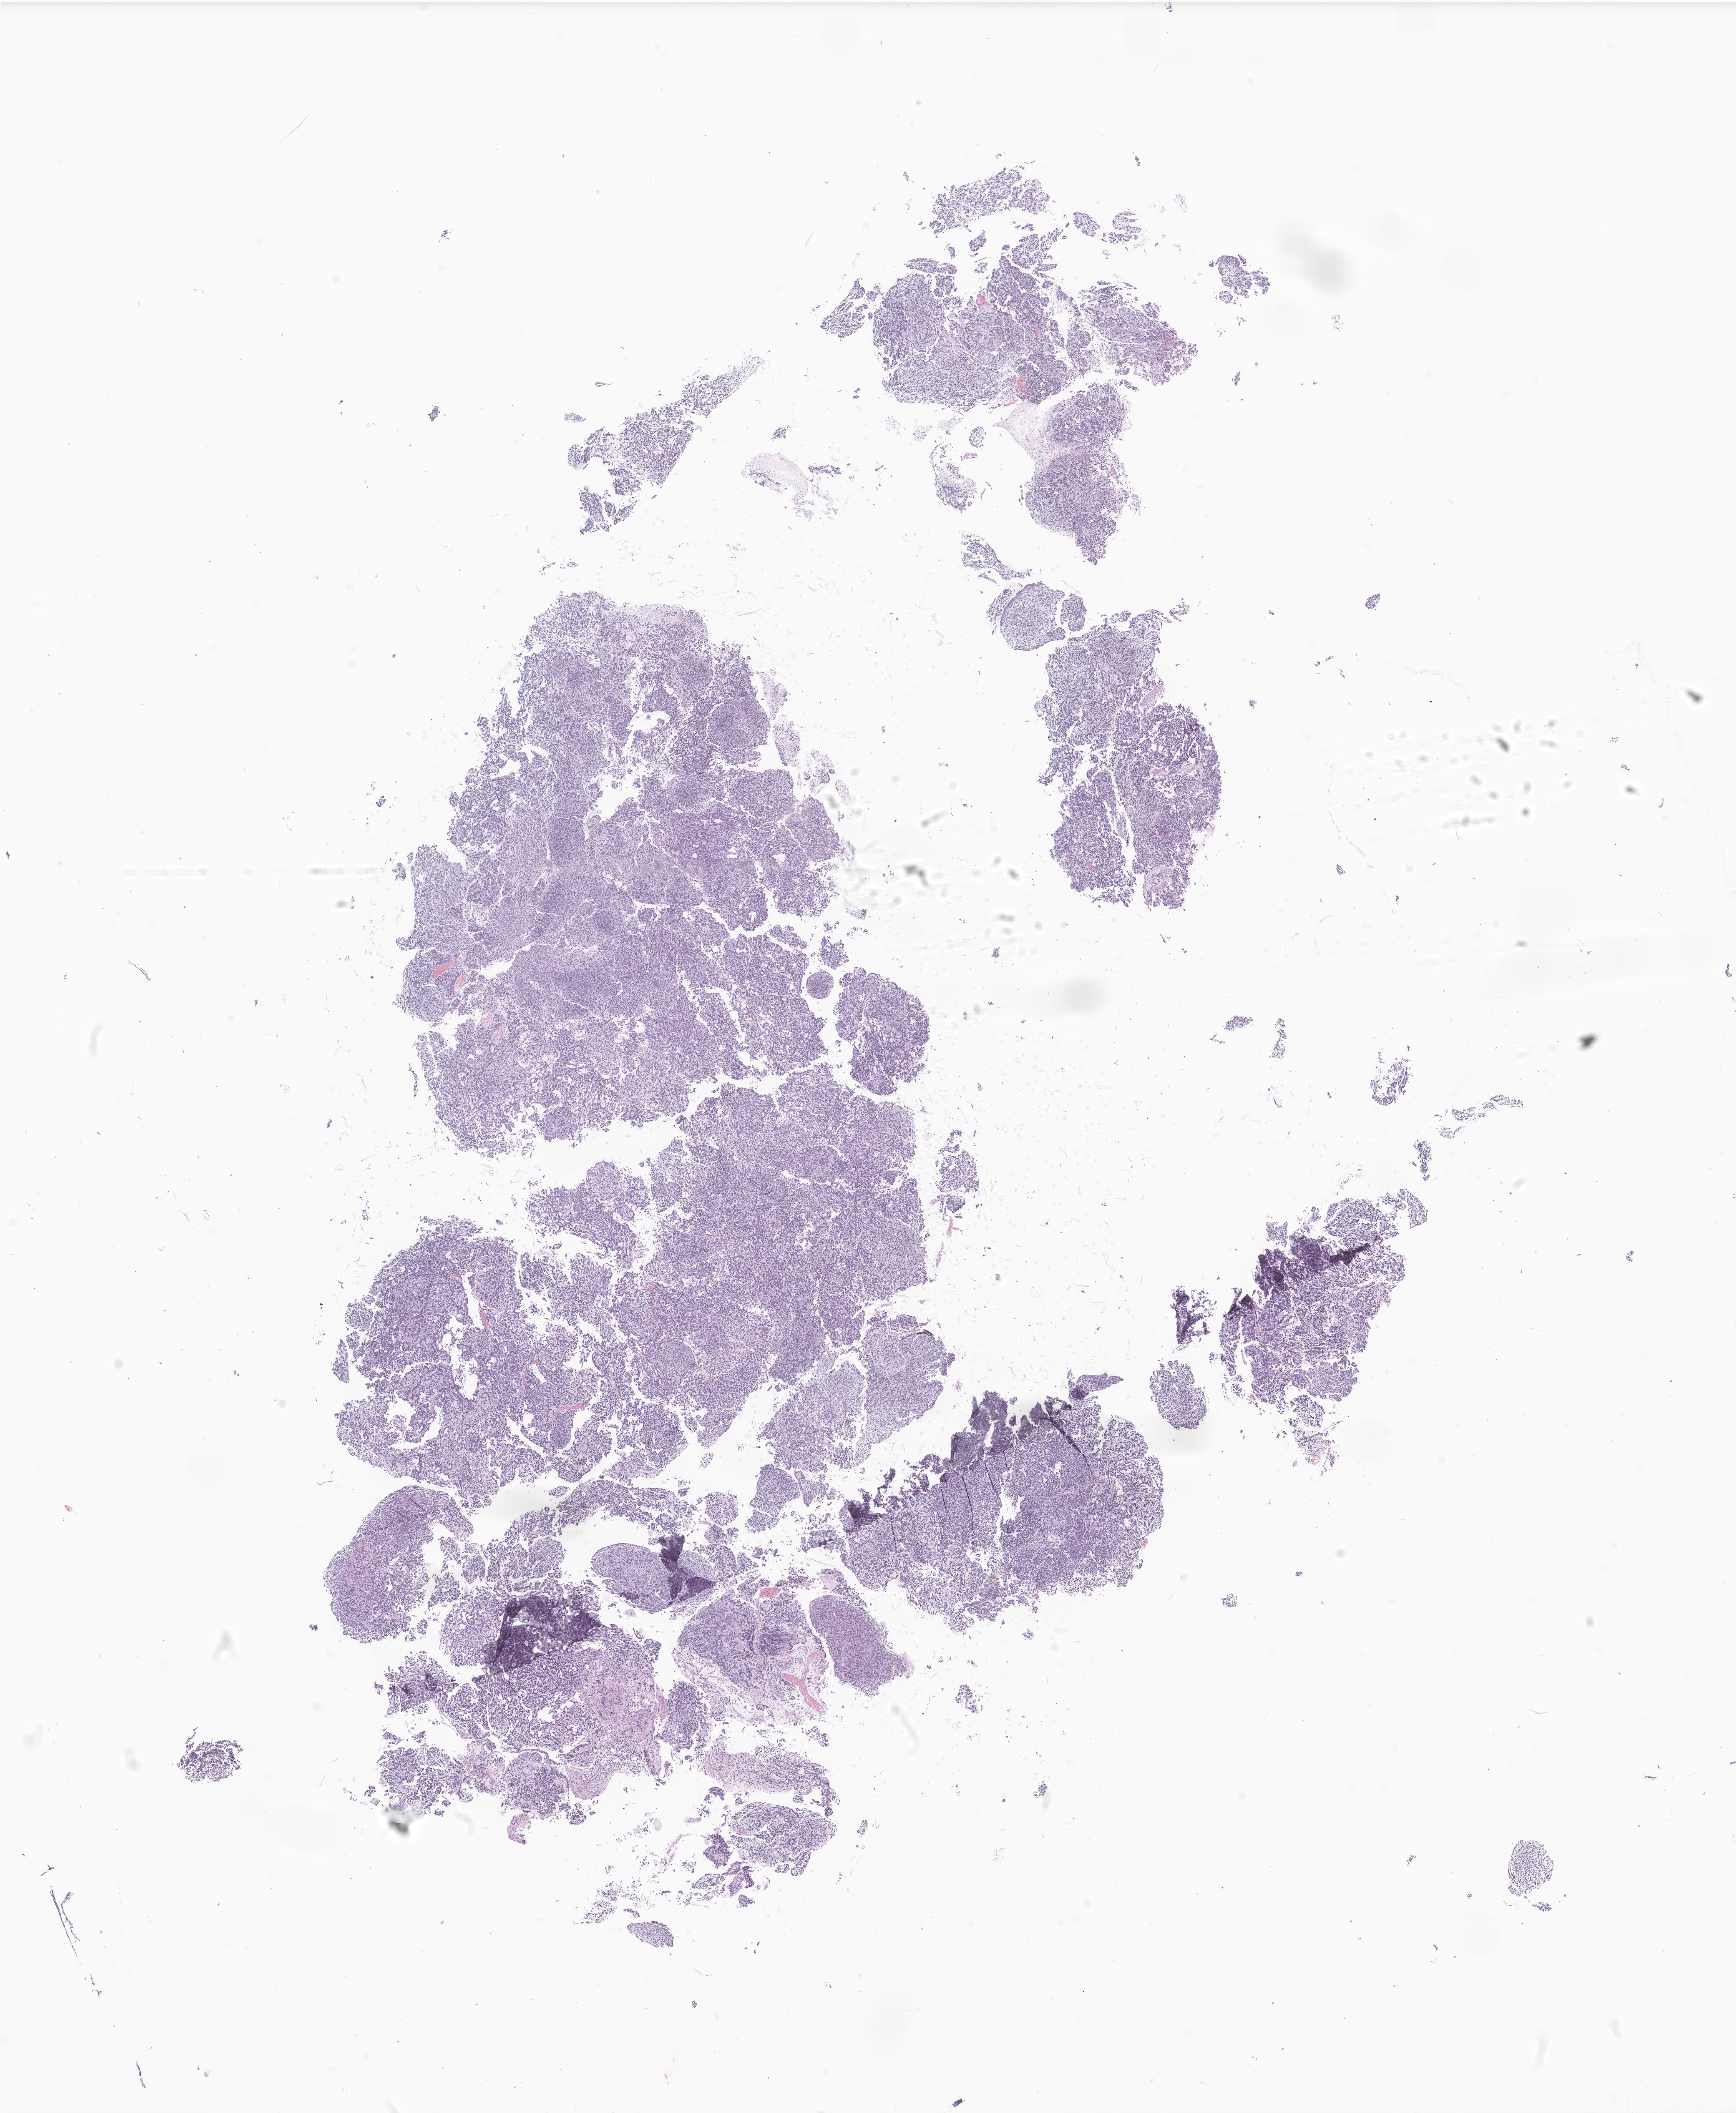
Haematoxylin and eosin whole-slide image of tumor tissue from the brain, a low-resolution overview of the entire scanned area, about 19.0 x 23.2 mm. Formalin-fixed paraffin-embedded section. Patient: female, age 86 months (7 years 2 months).
- diagnosis (ICD-O-3 morphology term): Medulloblastoma, NOS